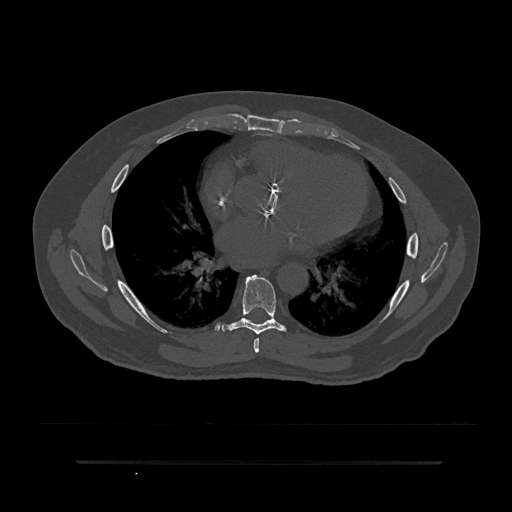
CT including the spine, one axial slice. Position 482 of 797 along the scan axis. 120 kVp. Bone window (W 1800 / L 400 HU). 0.5 mm slice thickness. 512 × 512 image matrix, field of view 464 × 464 mm. Patient: male, 59 years. From the clinical record (not read from this slice): primary cancer: bile ducts; vertebrae with lytic lesions (as recorded): T10.
Structures marked on this image (semi-automatic segmentation, software-assisted and operator-edited):
- T6 vertebra: bounding box <253,338,260,353> (left, top, right, bottom; pixels)
- T7 vertebra: <222,275,286,335>